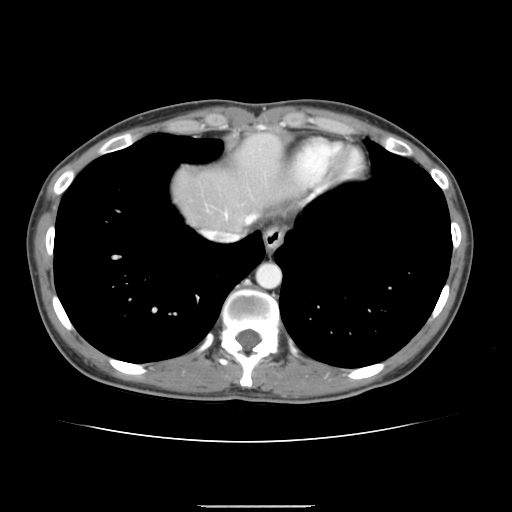
Contrast-enhanced abdominal CT, one axial slice. Position 133 of 150 along the scan axis. 120 kVp. Intravenous contrast given. Soft-tissue window (W 400 / L 40 HU). 512 × 512 image matrix, field of view 324 × 324 mm. Female patient, age 32 years. From the clinical record (not read from this slice): diagnosis: colorectal cancer liver metastases, imaged before liver resection; multiple liver metastases: yes; largest metastasis: 0.7 cm; chemotherapy before resection: yes.
Structures marked on this image (expert manual segmentation):
- hepatic veins: bounding box [x1, y1, x2, y2] px = [202, 214, 256, 241]
- liver: [173, 134, 295, 230]
- planned liver remnant (the part of the liver to remain after resection): [173, 134, 299, 231]